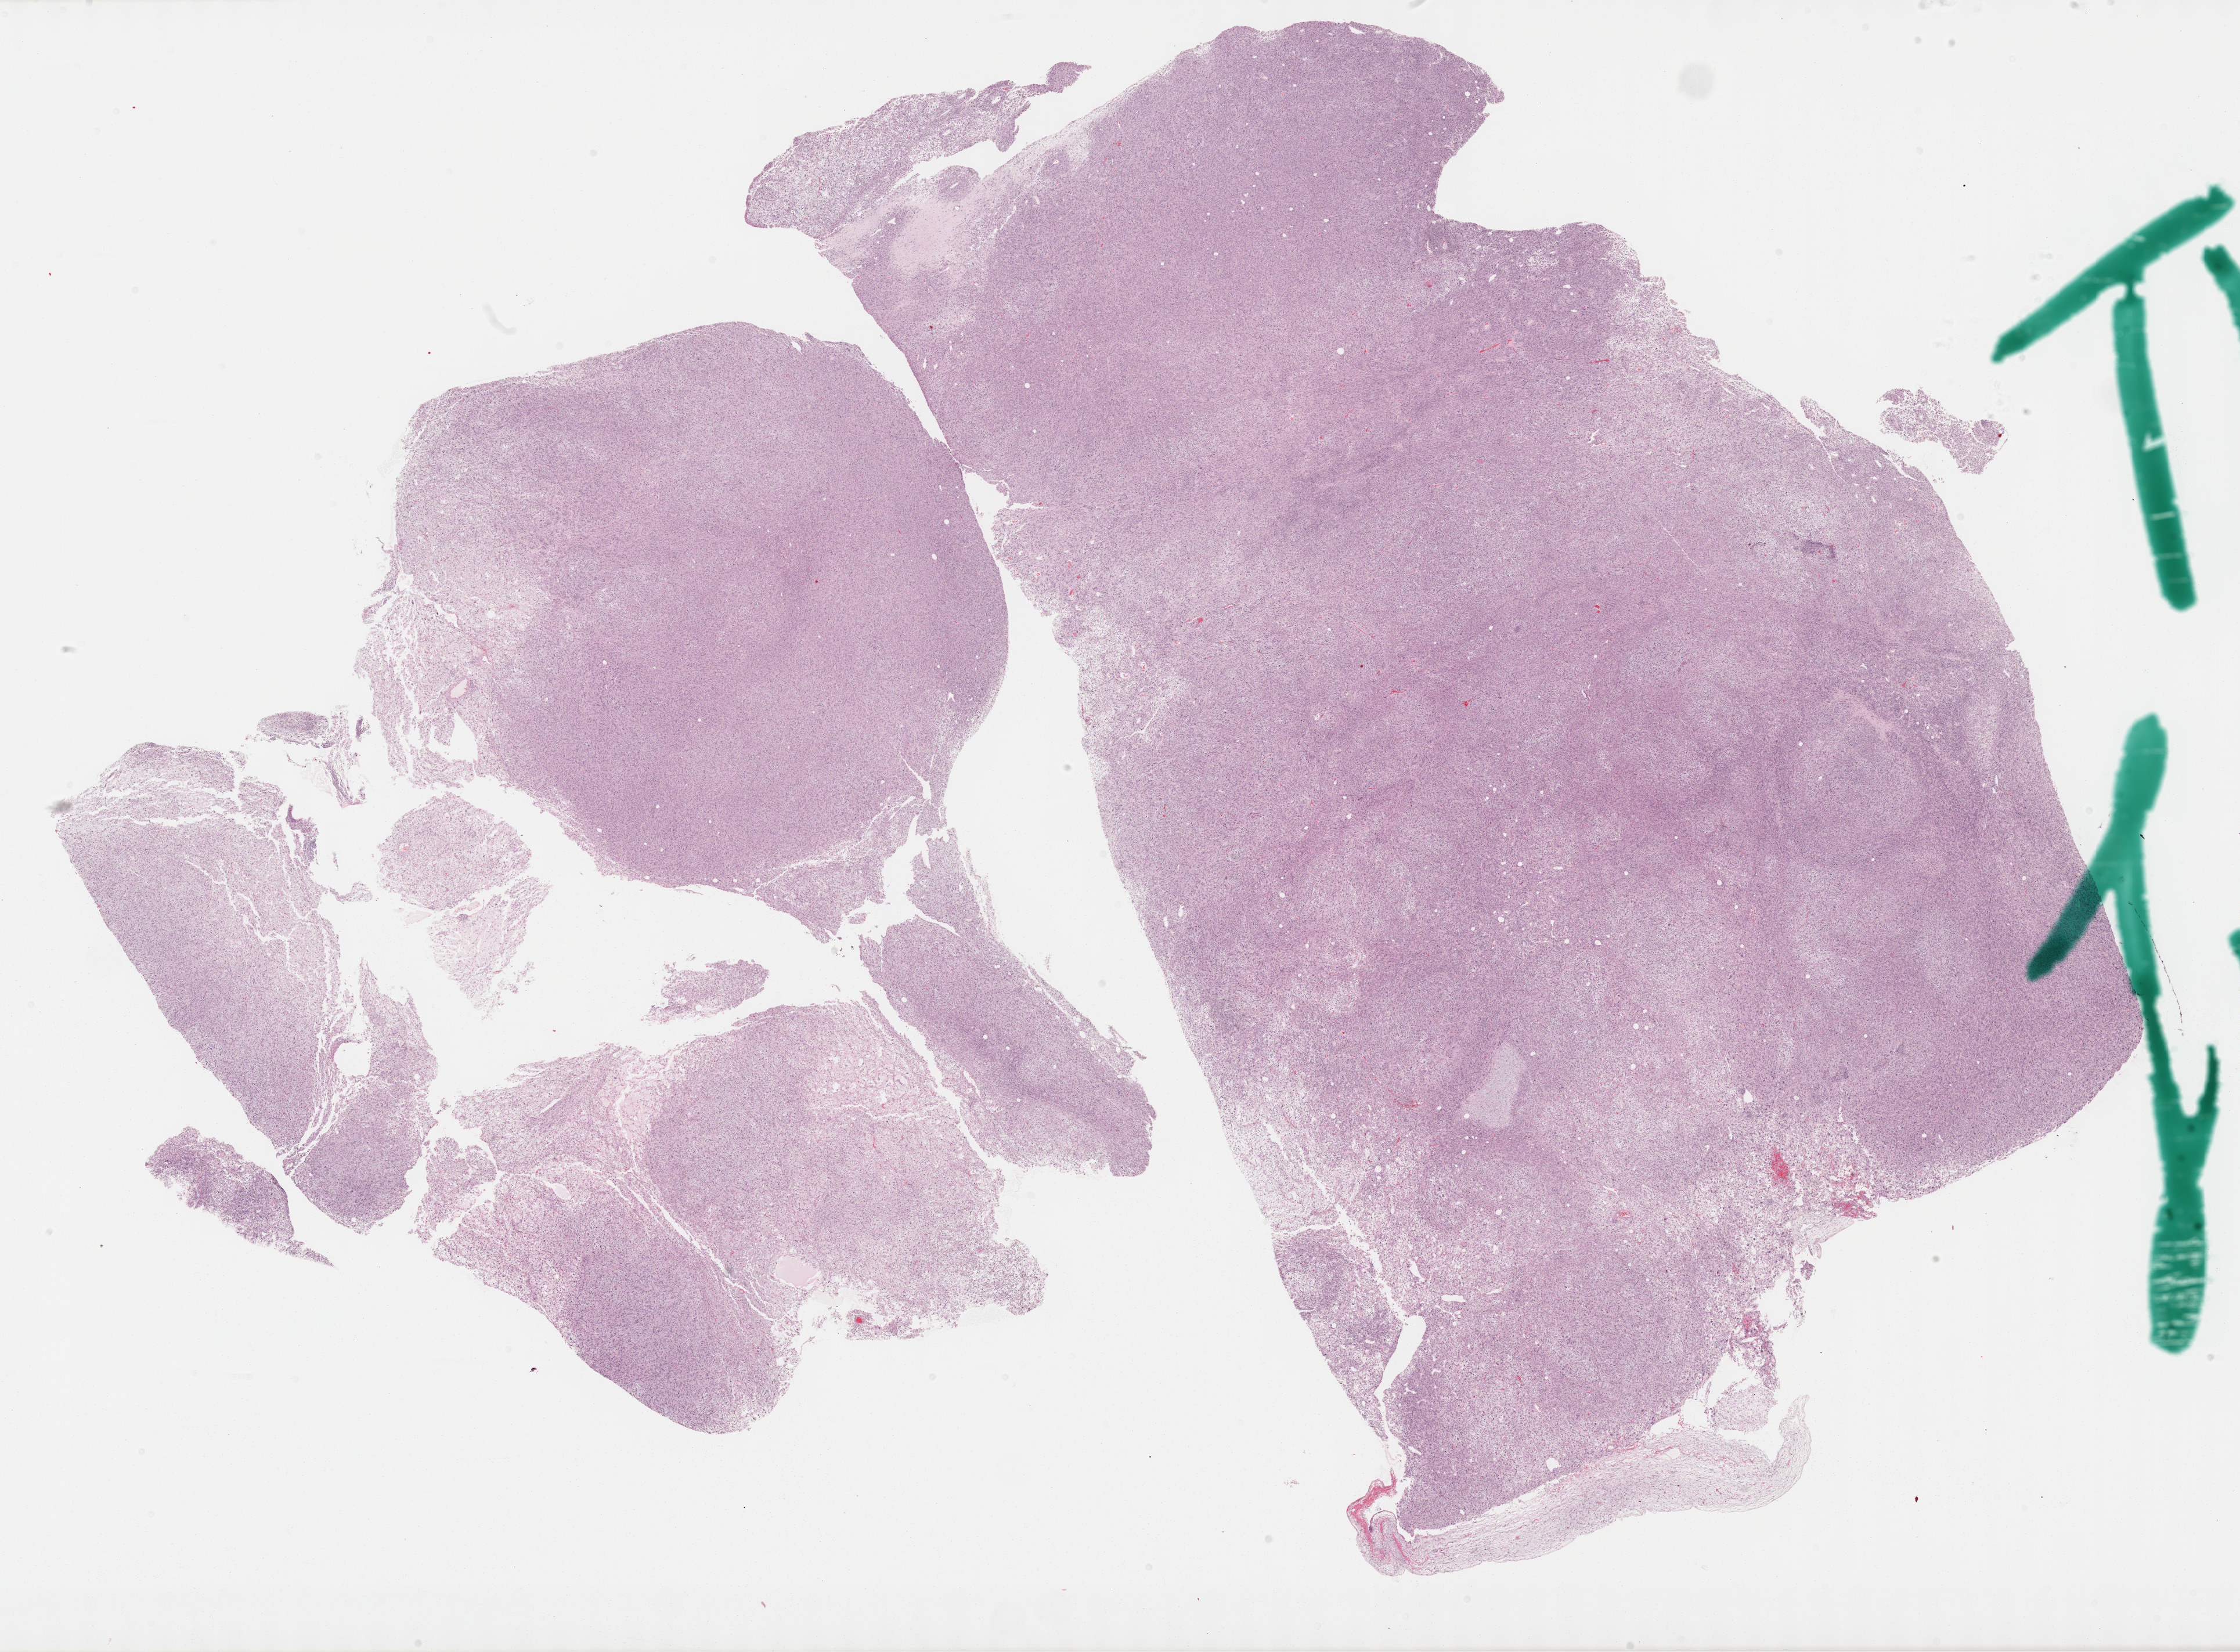
Whole-slide histology image, H&E — low-resolution overview of the scanned area, about 31.2 x 23.0 mm (from a 40x scan), formalin-fixed paraffin-embedded (FFPE) diagnostic section, sample: primary tumour, retroperitoneum and peritoneum. Male patient; age at initial diagnosis 78 years.
Histologic diagnosis: Dedifferentiated liposarcoma (retroperitoneum).